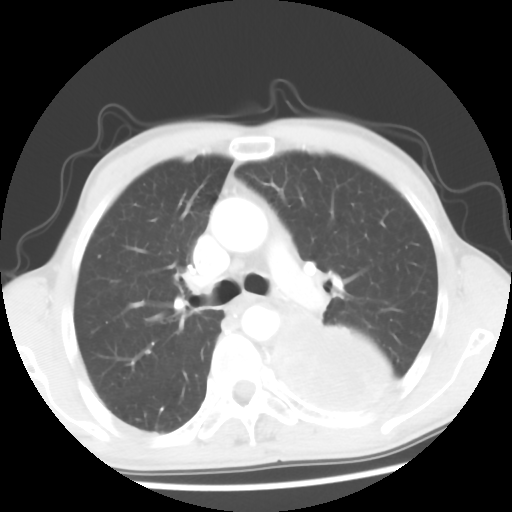
Chest CT, one axial slice. Slice 37 of 56 in the series (ordered by position). Reconstruction kernel STANDARD. 120 kVp. Lung window (W 1500 / L -600 HU). 5 mm slice thickness. 512 × 512 image matrix, field of view 318 × 318 mm. Male patient, age 60 years. Case-level facts recorded for this patient, not image findings: clinical TNM (as recorded): T4 N0 M0.
Annotated regions visible in this slice (bounding box drawn by a radiologist):
- lung tumour (recorded histology: squamous cell carcinoma): bounding box [x1, y1, x2, y2] px = [274, 302, 392, 424]